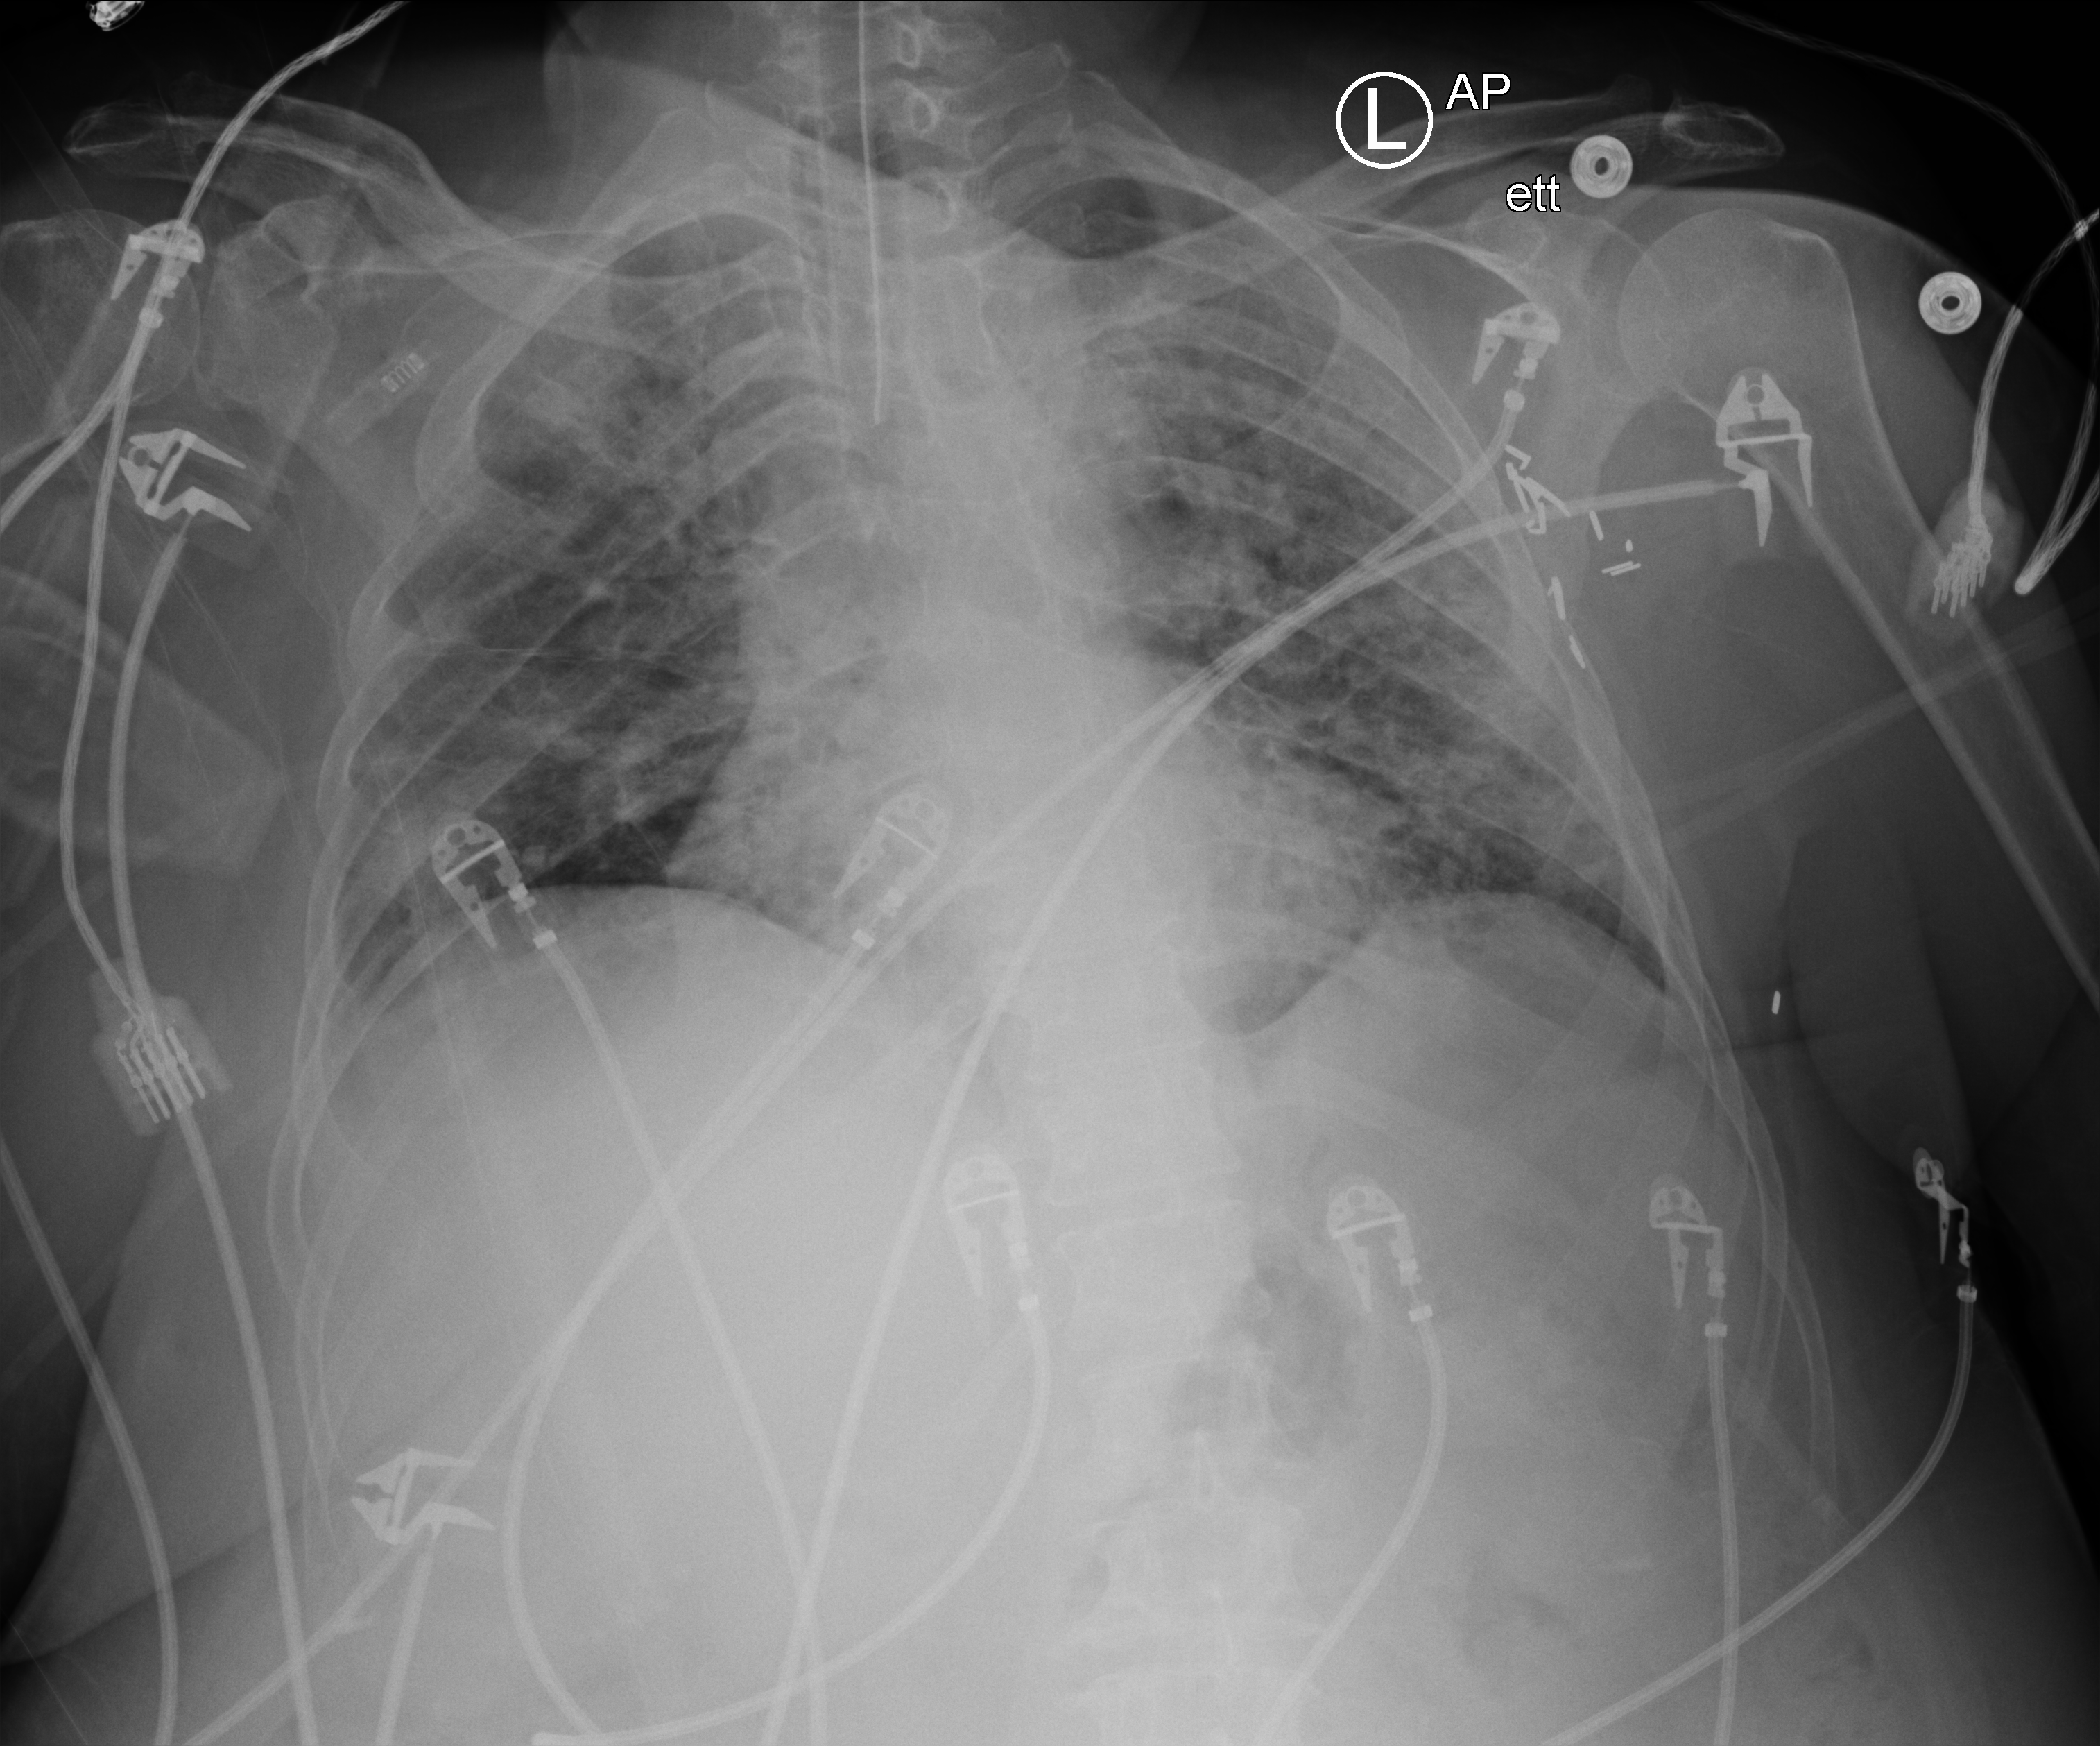
Portable chest radiograph; anteroposterior (AP) projection. Female patient hospitalised with COVID-19, age 60–74 years.
Admission-level facts for this patient (not findings on this image; timing relative to this image not recorded):
- chronic kidney disease (admission record): no
- admitted to intensive care during this hospital stay: yes